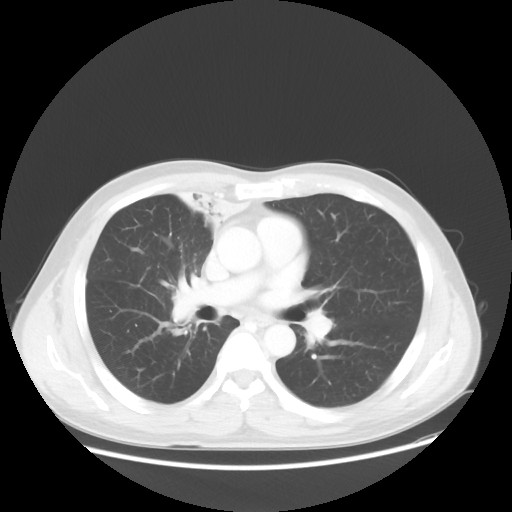
Chest CT, one axial slice. Position 30 of 56 along the scan axis. 100 kVp. Lung window (W 1500 / L -600 HU). 5 mm slice thickness. 512 × 512 image matrix, field of view 398 × 398 mm. Male patient, age 60 years. Case-level facts recorded for this patient, not image findings: clinical TNM (as recorded): T2a N1 M0.
Outlined on this slice (rectangle marked by the reading radiologist):
- lung tumour (recorded histology: squamous cell carcinoma): bounding box (x1, y1, x2, y2) in pixels: (170, 174, 247, 240)